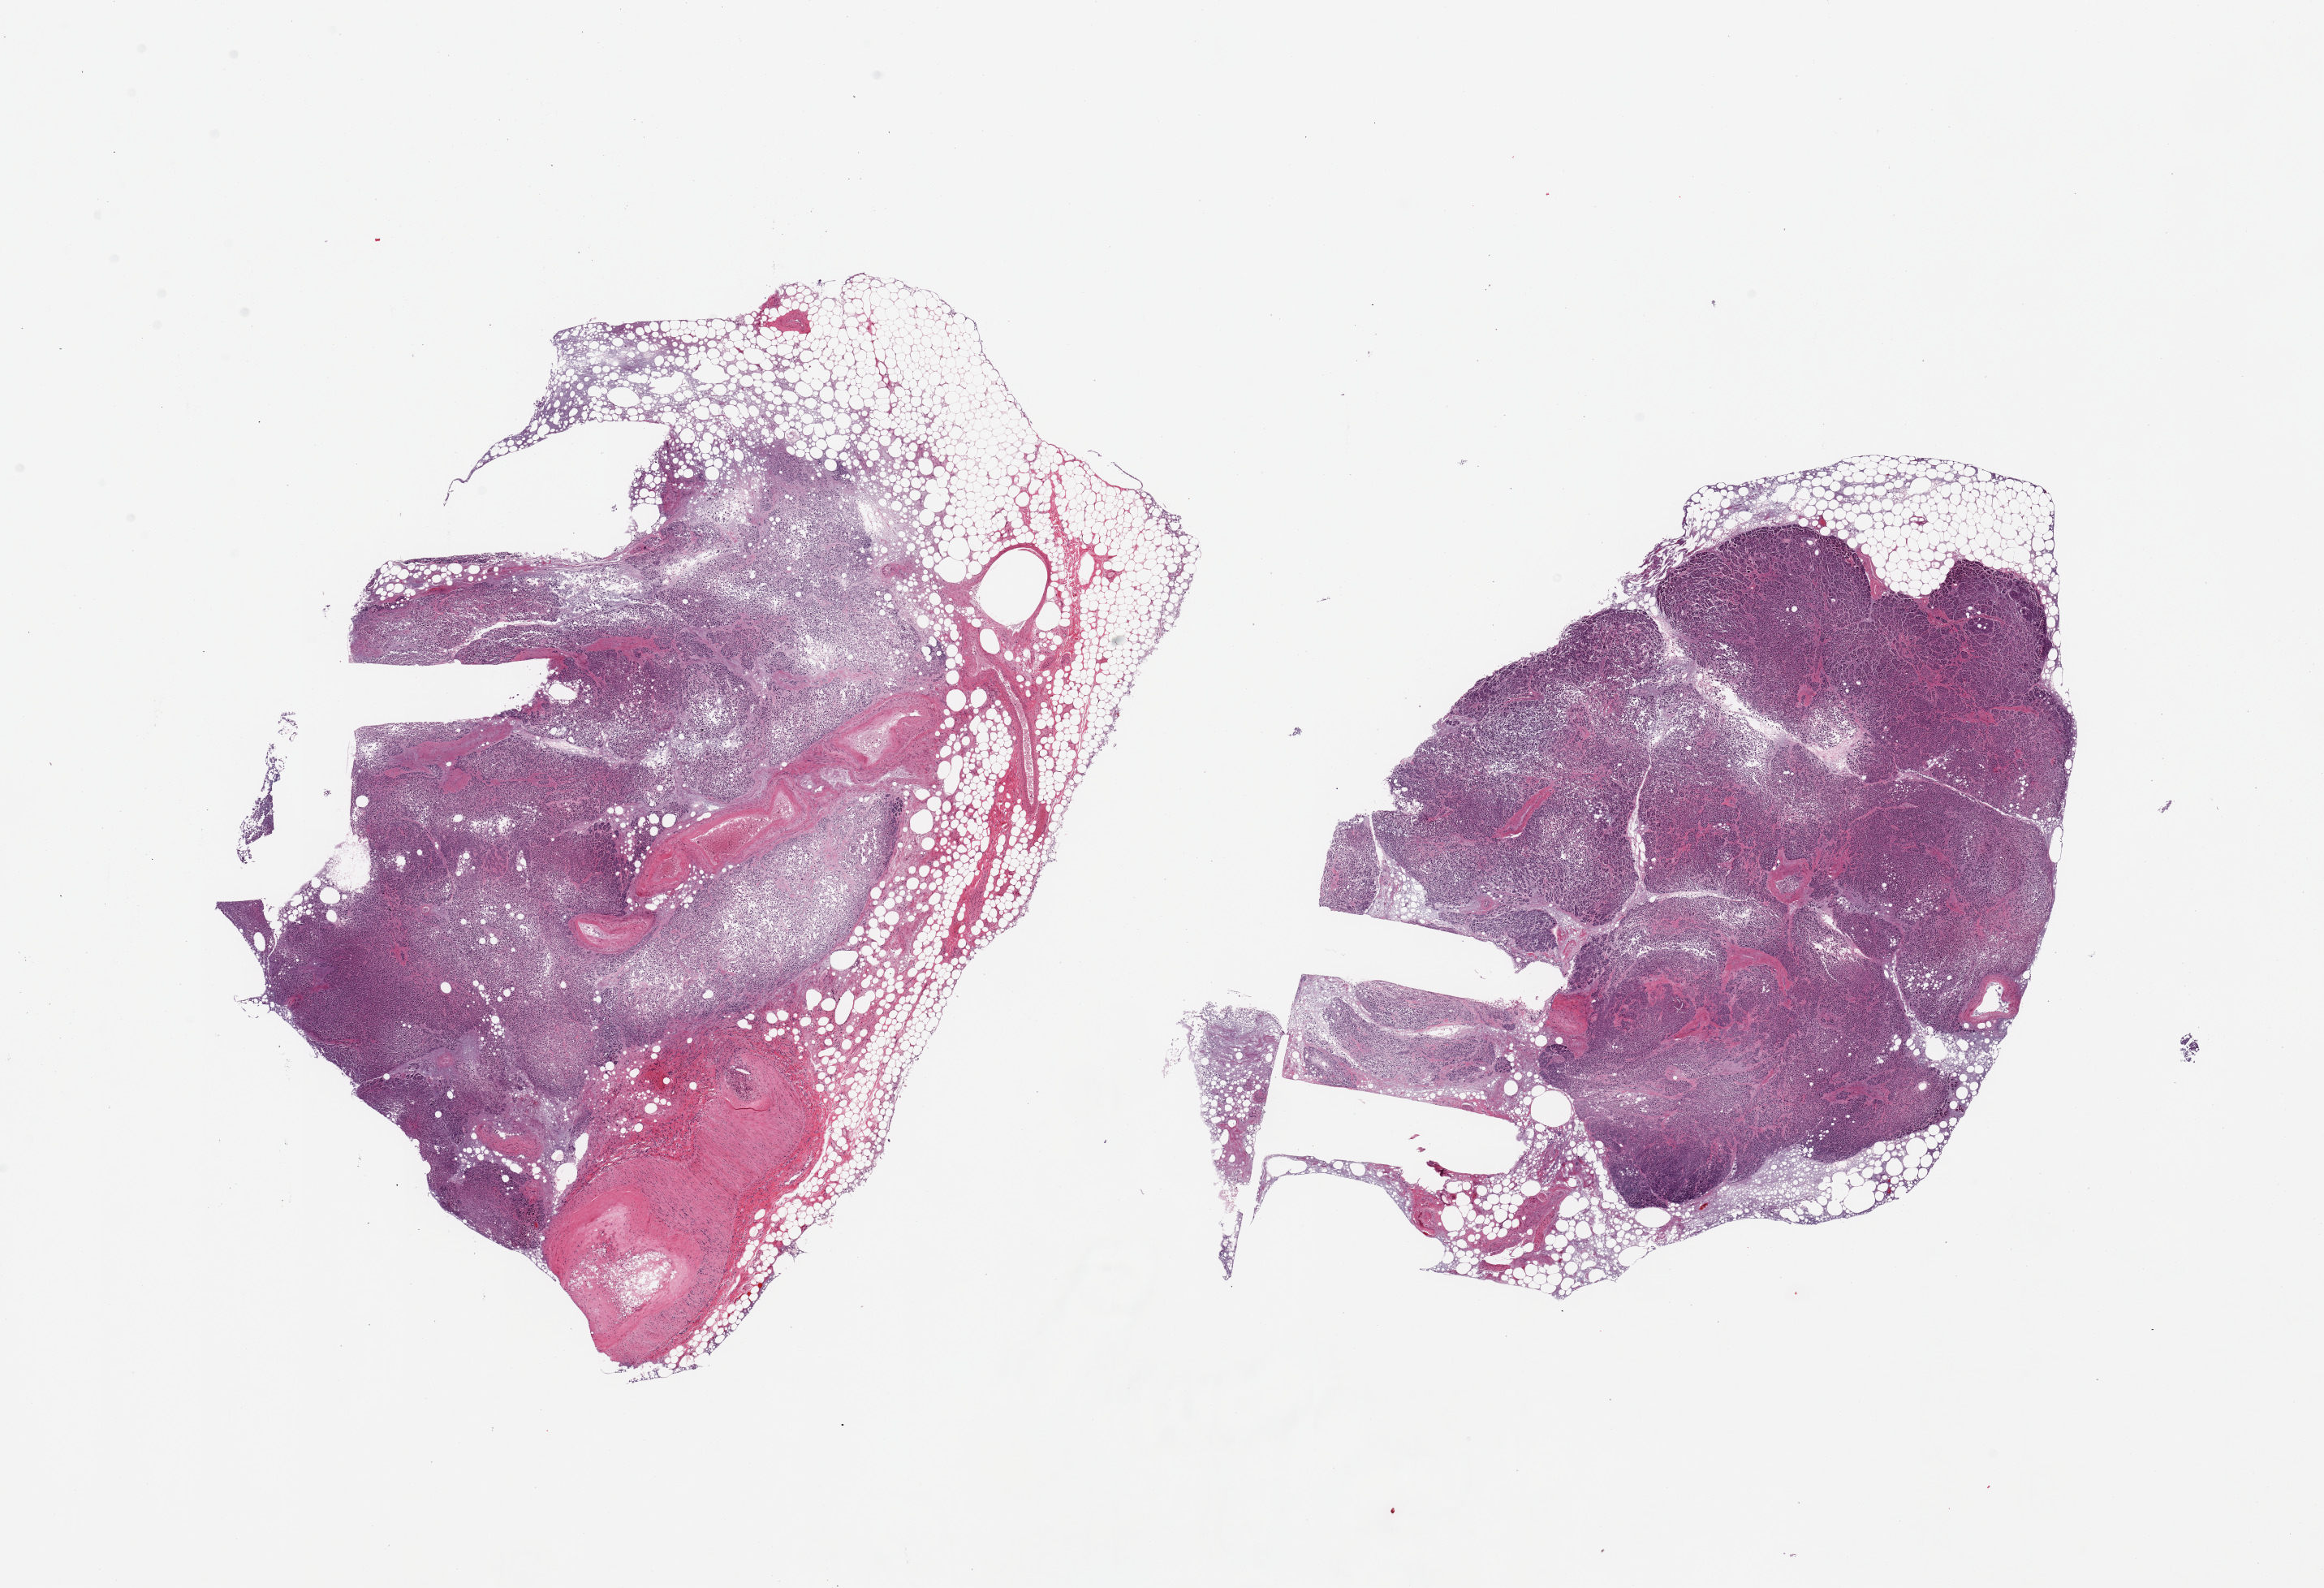
Whole-slide image, hematoxylin and eosin (H&E) stain — low-resolution overview of the scanned area, about 22.6 x 15.5 mm. PAXgene-fixed paraffin-embedded (PFPE) section. Target tissue: pancreas. Donor tissue sample. Male donor.
Pathologist's review note for this sample: 2 pieces, advanced autolysis/saponification, Islets not visualized.